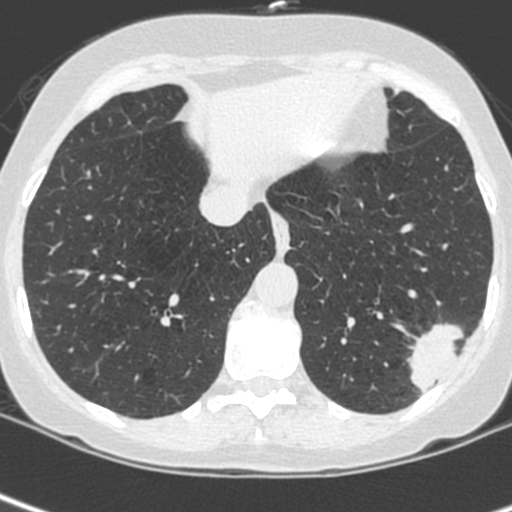
Axial slice from a low-dose chest CT screening exam, first (baseline) screen, lung window (W 1500 / L -600 HU), 1.3 mm slice thickness, 512 × 512 image matrix. Female participant, aged 56 years at enrolment. Current smoker at enrolment.
Expert-annotated lung lesion, box from (x=404, y=314) to (x=477, y=388) px. Screening reader's record for this exam (one nodule recorded; not confirmed to be the boxed lesion): non-calcified nodule or mass ≥4 mm, left lower lobe, 37 × 29 mm, spiculated (stellate) margins, ground glass attenuation.